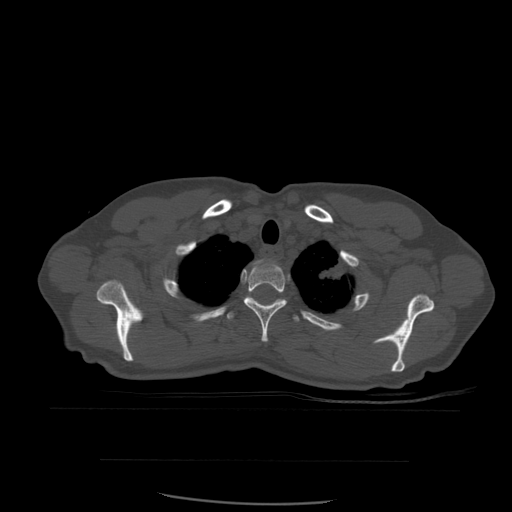
CT including the spine, one axial slice; slice 455 of 574 in the series (ordered by position); bone window (W 1800 / L 400 HU); 512 × 512 image matrix, field of view 392 × 392 mm. Patient age 48 years. From the clinical record (not read from this slice): primary cancer: lung.
Structures marked on this image (semi-automatic segmentation, software-assisted and operator-edited):
- T1 vertebra: bounding box (x1, y1, x2, y2) in pixels: (253, 261, 259, 266)
- T2 vertebra: (244, 260, 287, 343)
- T3 vertebra: (227, 296, 300, 323)